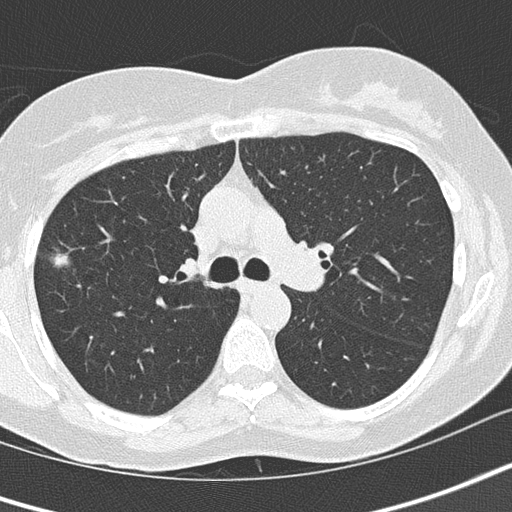
Chest CT (low-dose screening protocol), one axial image, baseline annual screen, lung window (W 1500 / L -600 HU), 2 mm slice thickness, 512 × 512 image matrix. Female participant, aged 64 years at enrolment. Former smoker at enrolment.
• Expert reader's lesion annotation, bounding box <31,234,83,285> (left, top, right, bottom; pixels).
• The screening reader recorded 4 non-calcified nodules or masses ≥4 mm on this exam; which of them this box marks is not recorded.
• Official screen result: positive, change unspecified: nodule(s) >= 4 mm or enlarging nodule(s), mass(es), or other non-specific abnormalities suspicious for lung cancer.
• Lung cancer was diagnosed 447 days after this screen: bronchiolo-alveolar adenocarcinoma, NOS, right upper lobe, well differentiated (G1), stage IA (AJCC 6th edition), 10 mm at pathology.